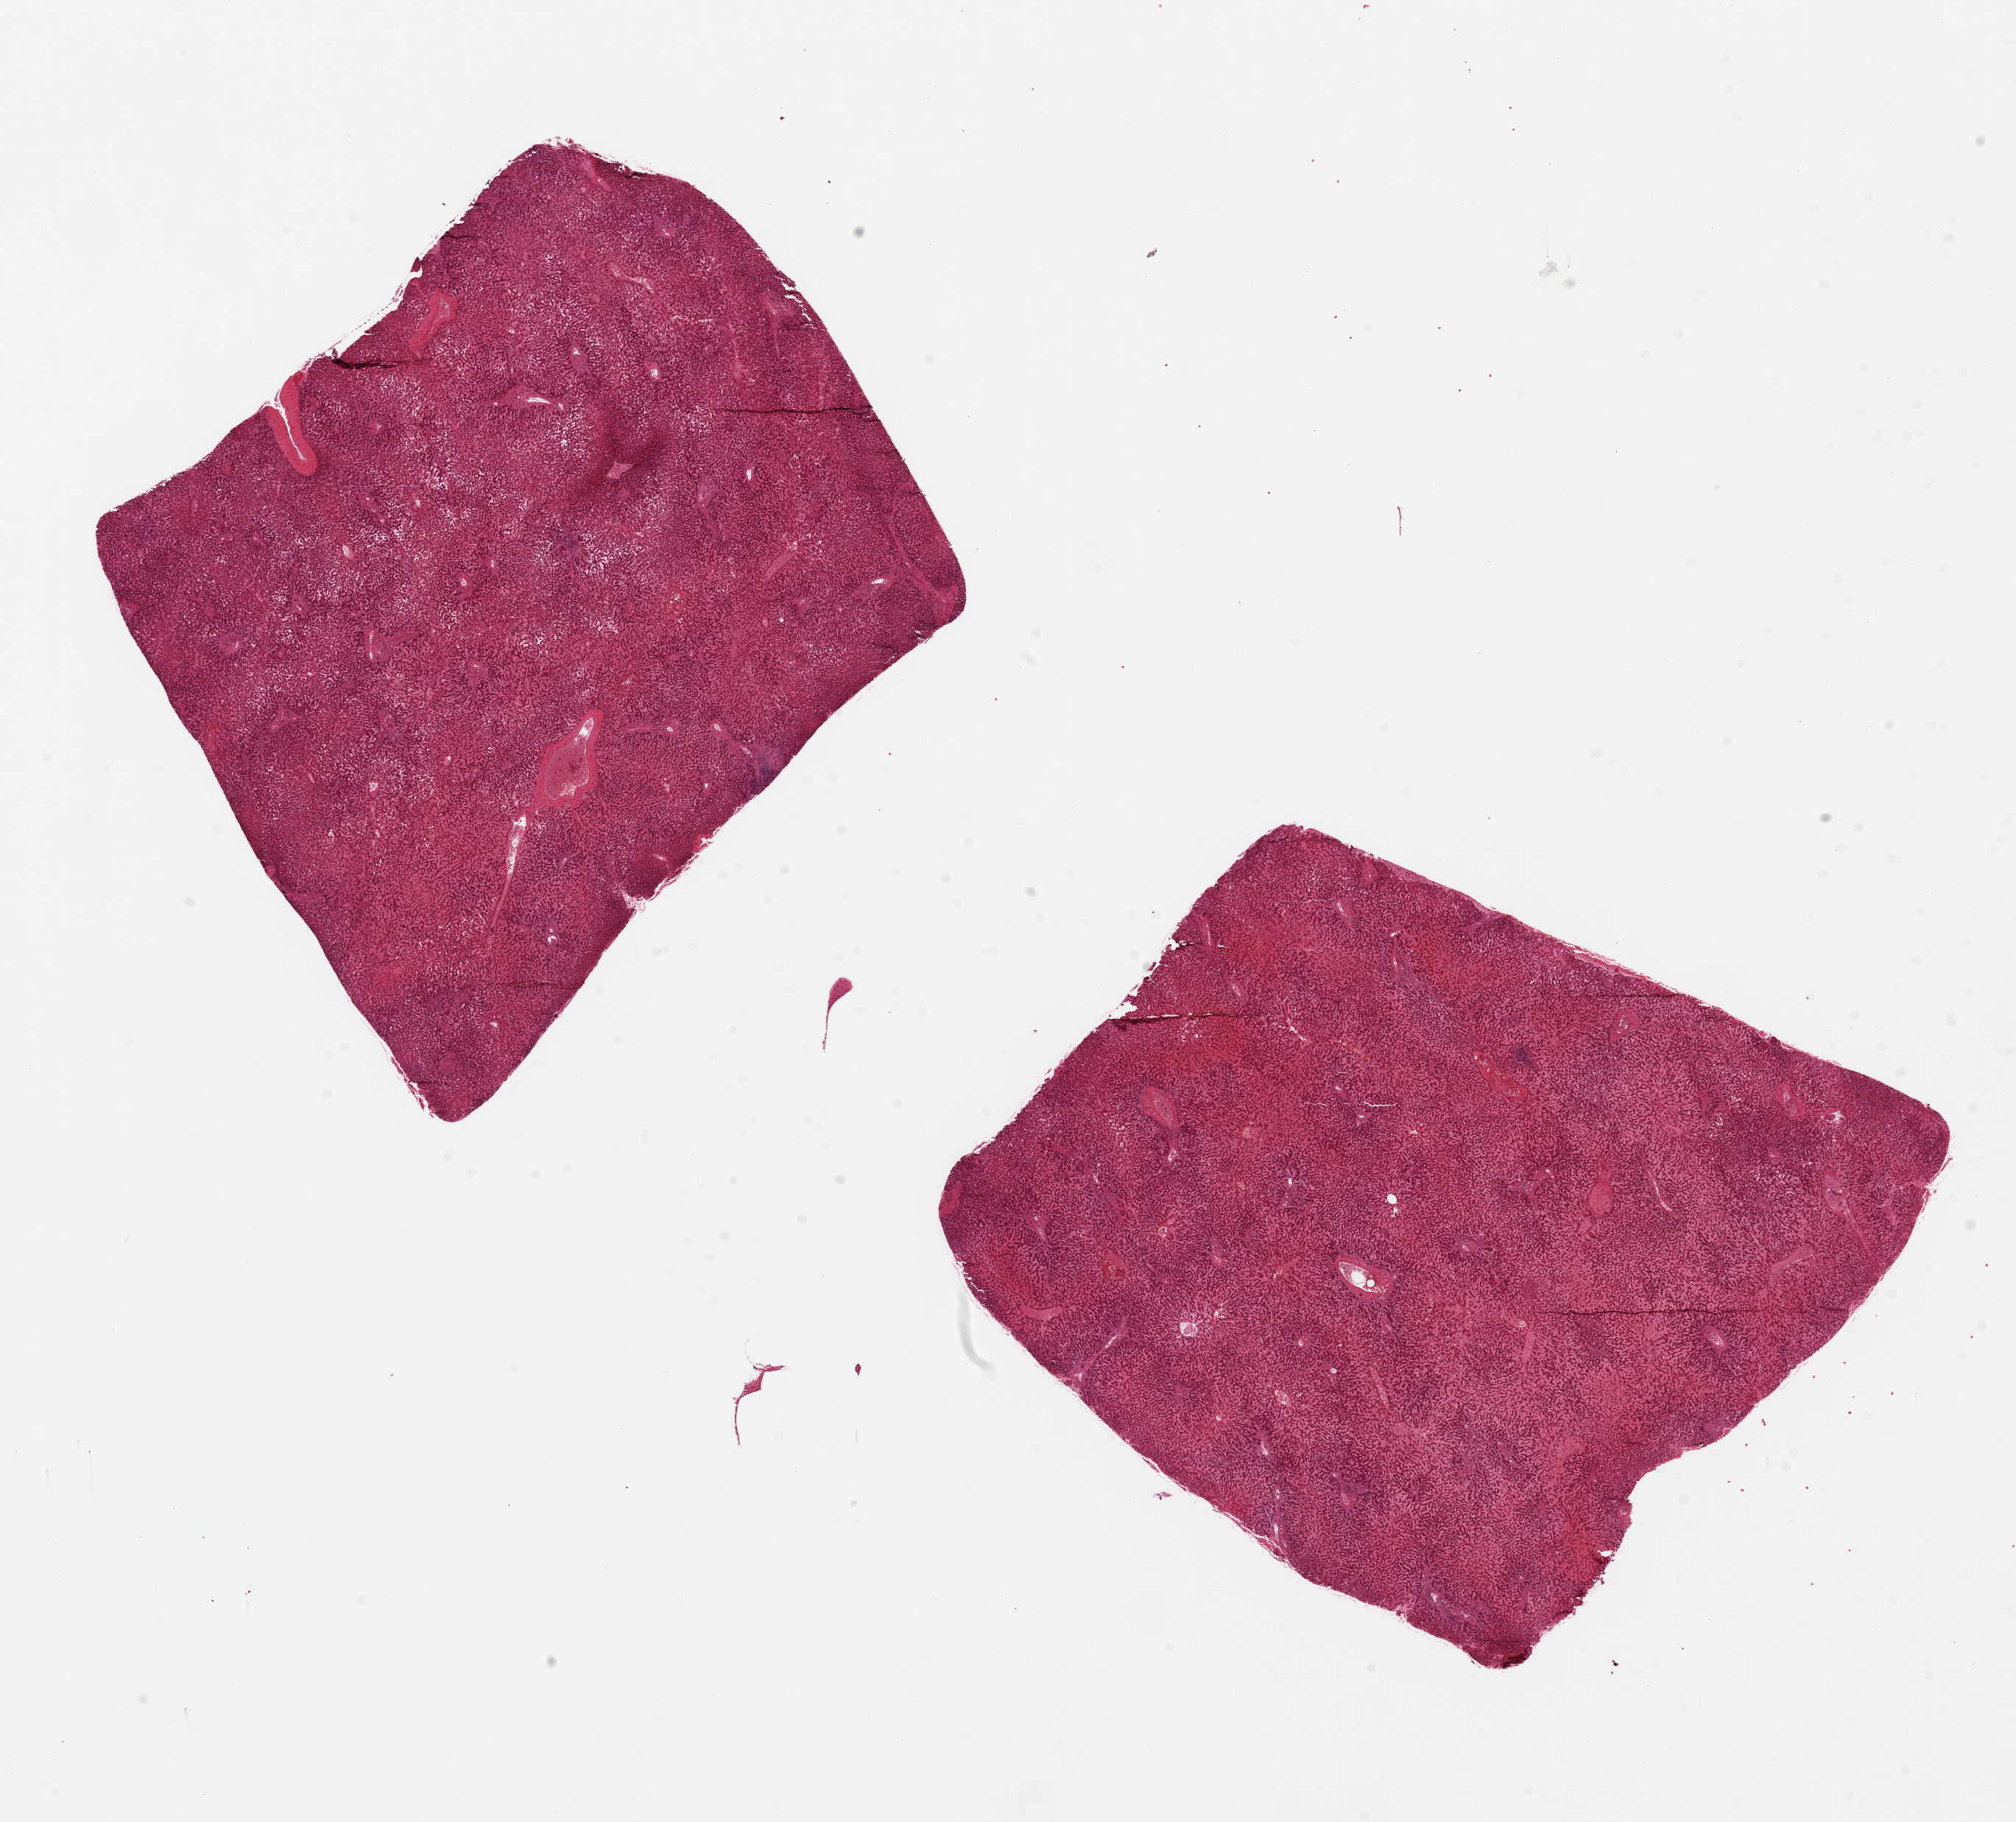
Whole-slide image, hematoxylin and eosin (H&E) stain, brightfield, a low-resolution overview of the entire scanned area, about 21.7 x 19.6 mm. PAXgene-fixed, paraffin-embedded tissue. Target tissue: liver. Tissue donor sample. Male donor.
* pathologist's review note for this sample: 2 pieces 8x7 & 8x6 mm; moderate central congestion